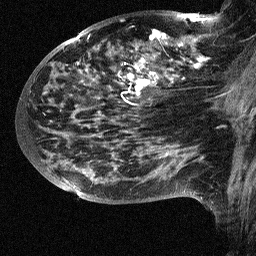
Breast MRI (dynamic contrast-enhanced), one sagittal slice; slice 36 of 64 in the series (ordered by position); dynamic contrast-enhanced study with each time point stored as its own series, time point 2 of 3 at this slice position (early post-contrast, ordered by acquisition time); 1.5 T; TE 4.5 ms, TR 11 ms; 2.5 mm slice thickness; 256 × 256 image matrix, field of view 200 × 200 mm. Patient: female, 38 years. From the clinical record (not read from this slice): setting: breast cancer imaged before/during neoadjuvant chemotherapy; receptor status: HR-positive, HER2-negative.
Outlined on this slice (semi-automatic segmentation, software-assisted and operator-edited):
- analysis volume of interest (the breast-tissue region the enhancement analysis was run in; not a lesion): bounding box [x1, y1, x2, y2] px = [88, 18, 252, 126]
- tumour enhancement mask (voxels above the 90 % enhancement threshold inside the analysis volume of interest): [120, 18, 207, 96]